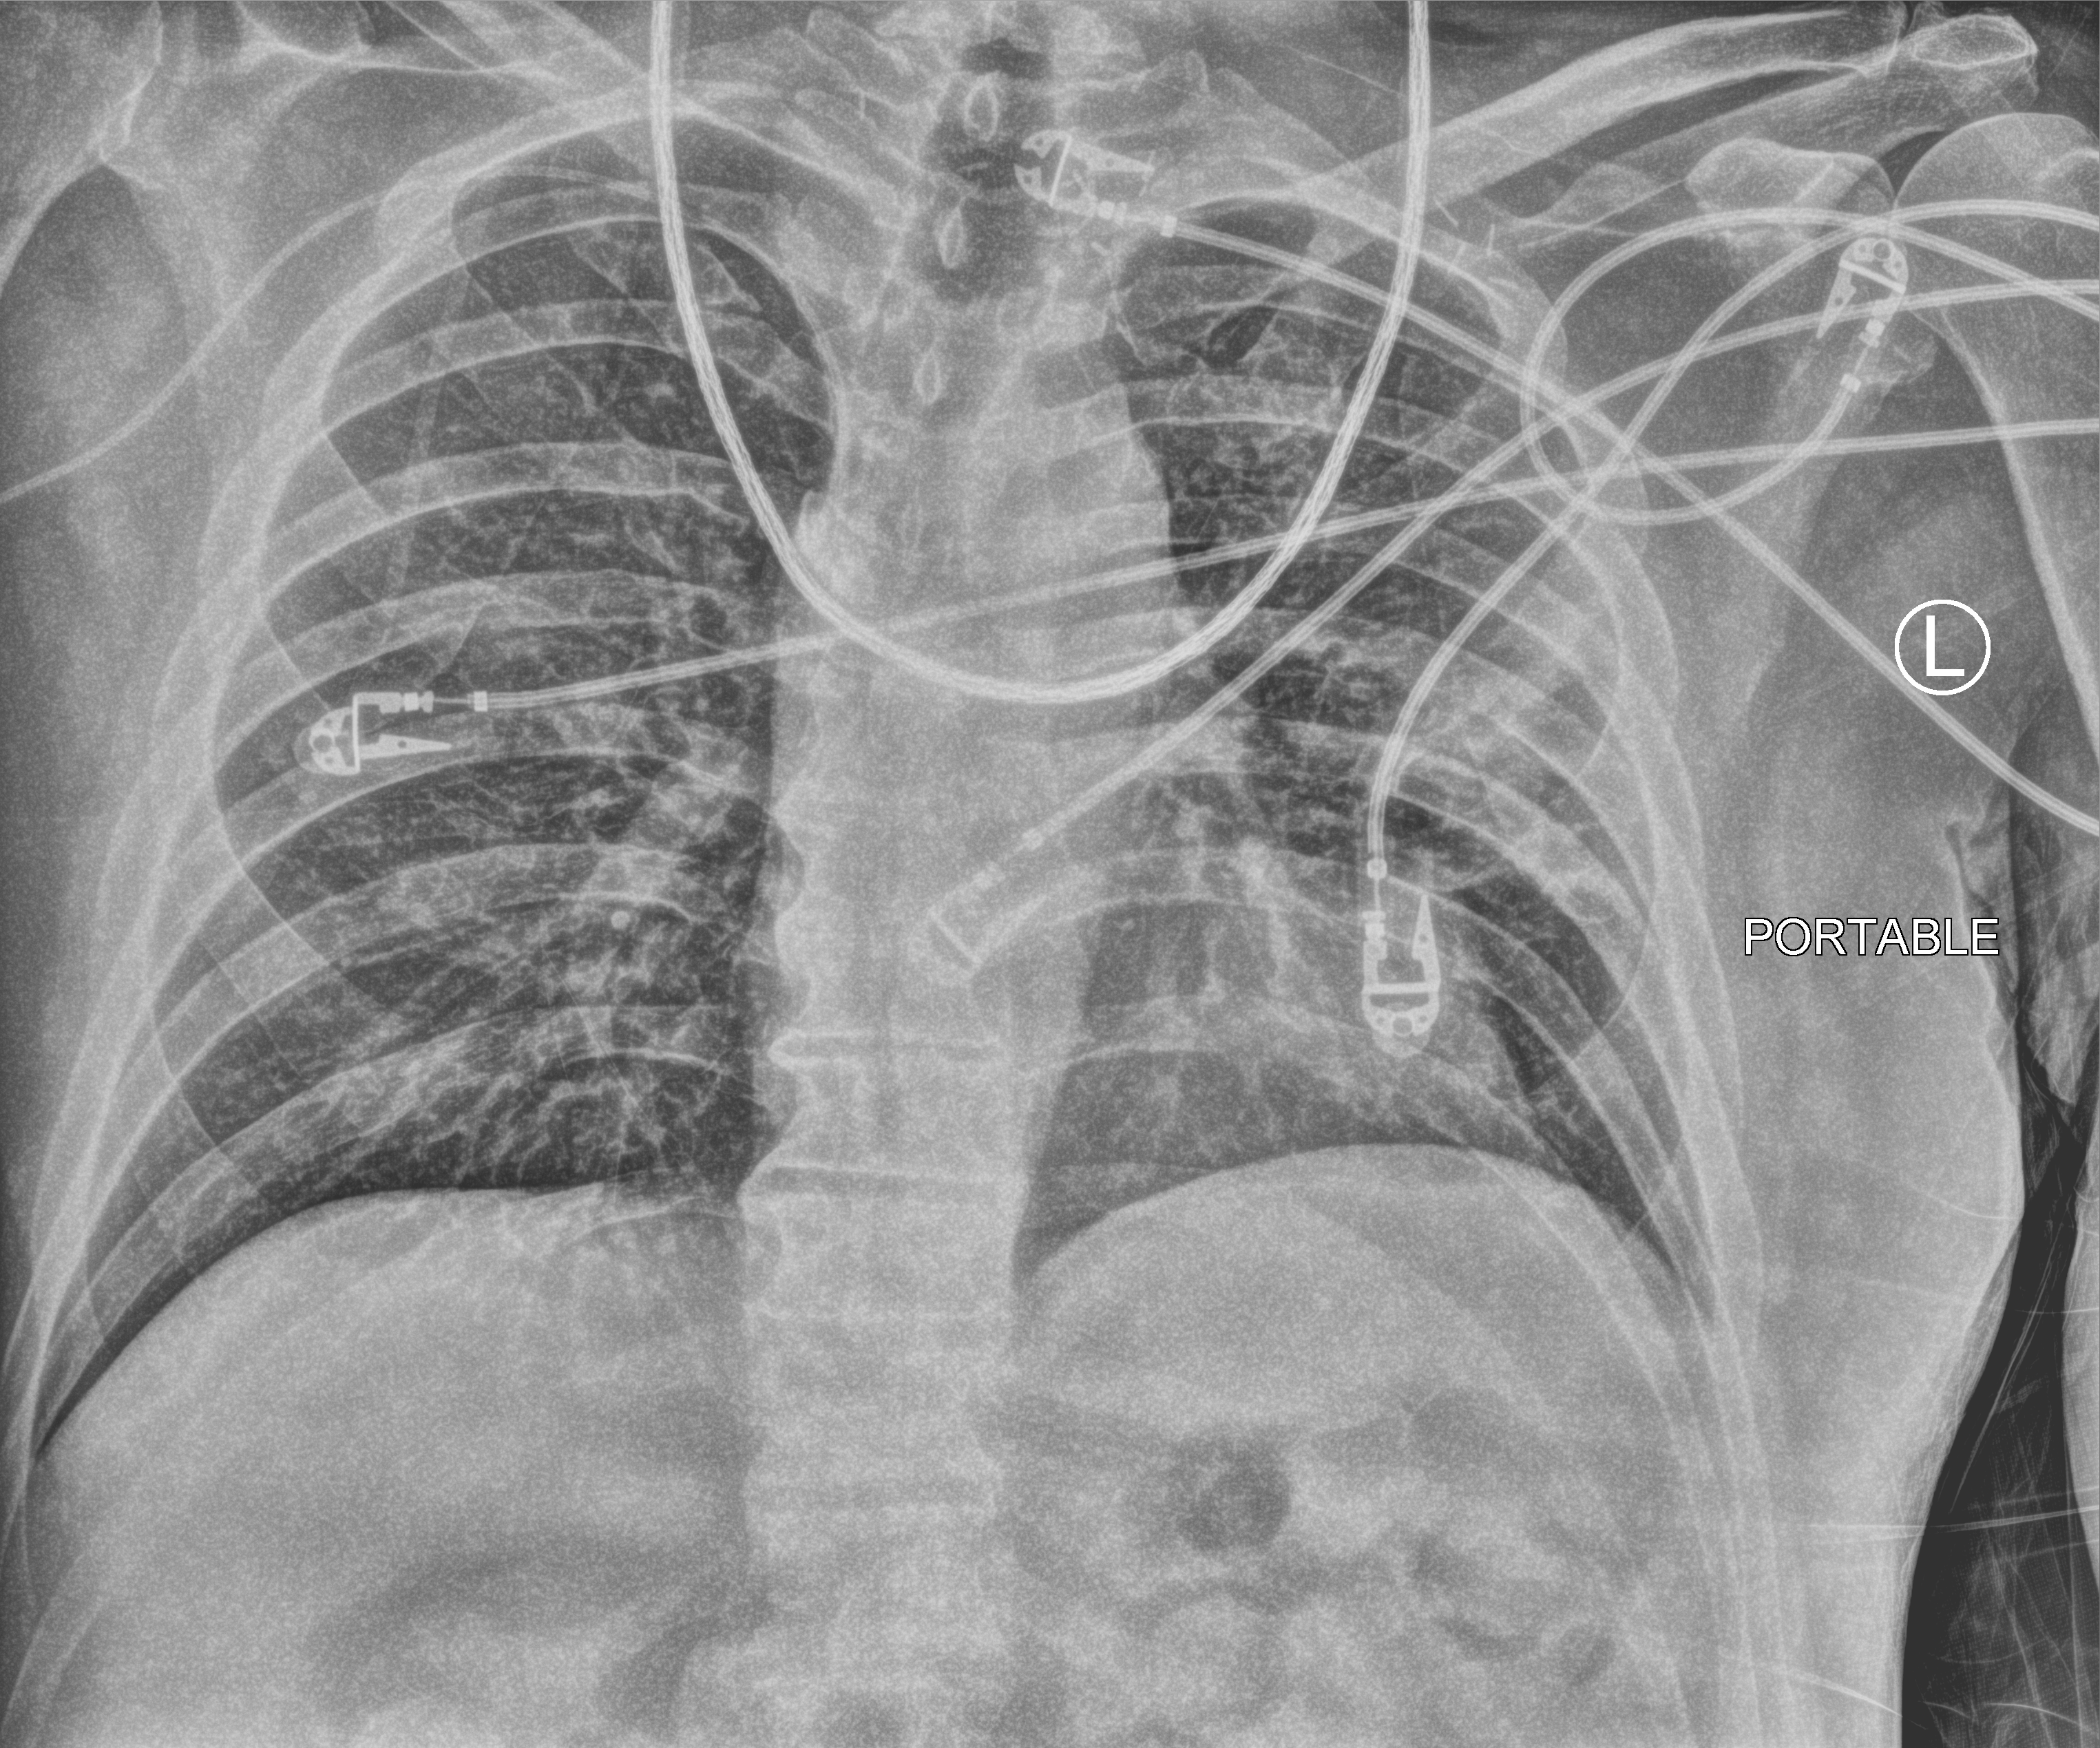
Bedside chest radiograph (computed radiography). Adult patient hospitalised with COVID-19, age 18–59 years.
From the hospital-stay record, not from the radiograph (when in the stay this image was taken is not recorded): admitted to intensive care during this hospital stay: yes; mechanically ventilated during this hospital stay: yes.